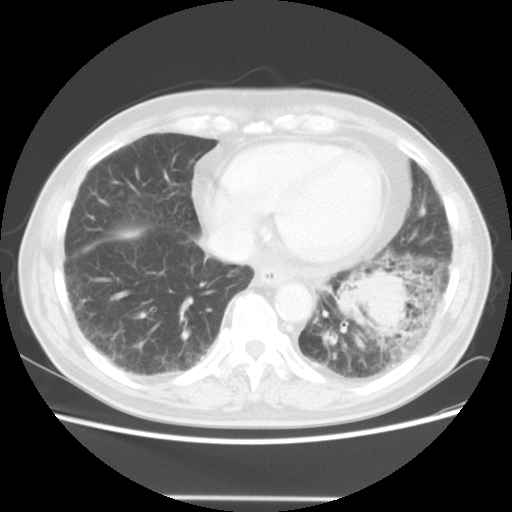
Chest CT, one axial slice; position 14 of 56 along the scan axis; 140 kVp; lung window (W 1500 / L -600 HU); 5 mm slice thickness; 512 × 512 image matrix. Male patient, age 66 years. From the clinical record (not read from this slice): clinical TNM (as recorded): T4 N3 M0.
Structures marked on this image (rectangle marked by the reading radiologist):
- lung tumour (recorded histology: small cell carcinoma): bounding box (x1, y1, x2, y2) in pixels: (331, 259, 422, 356)